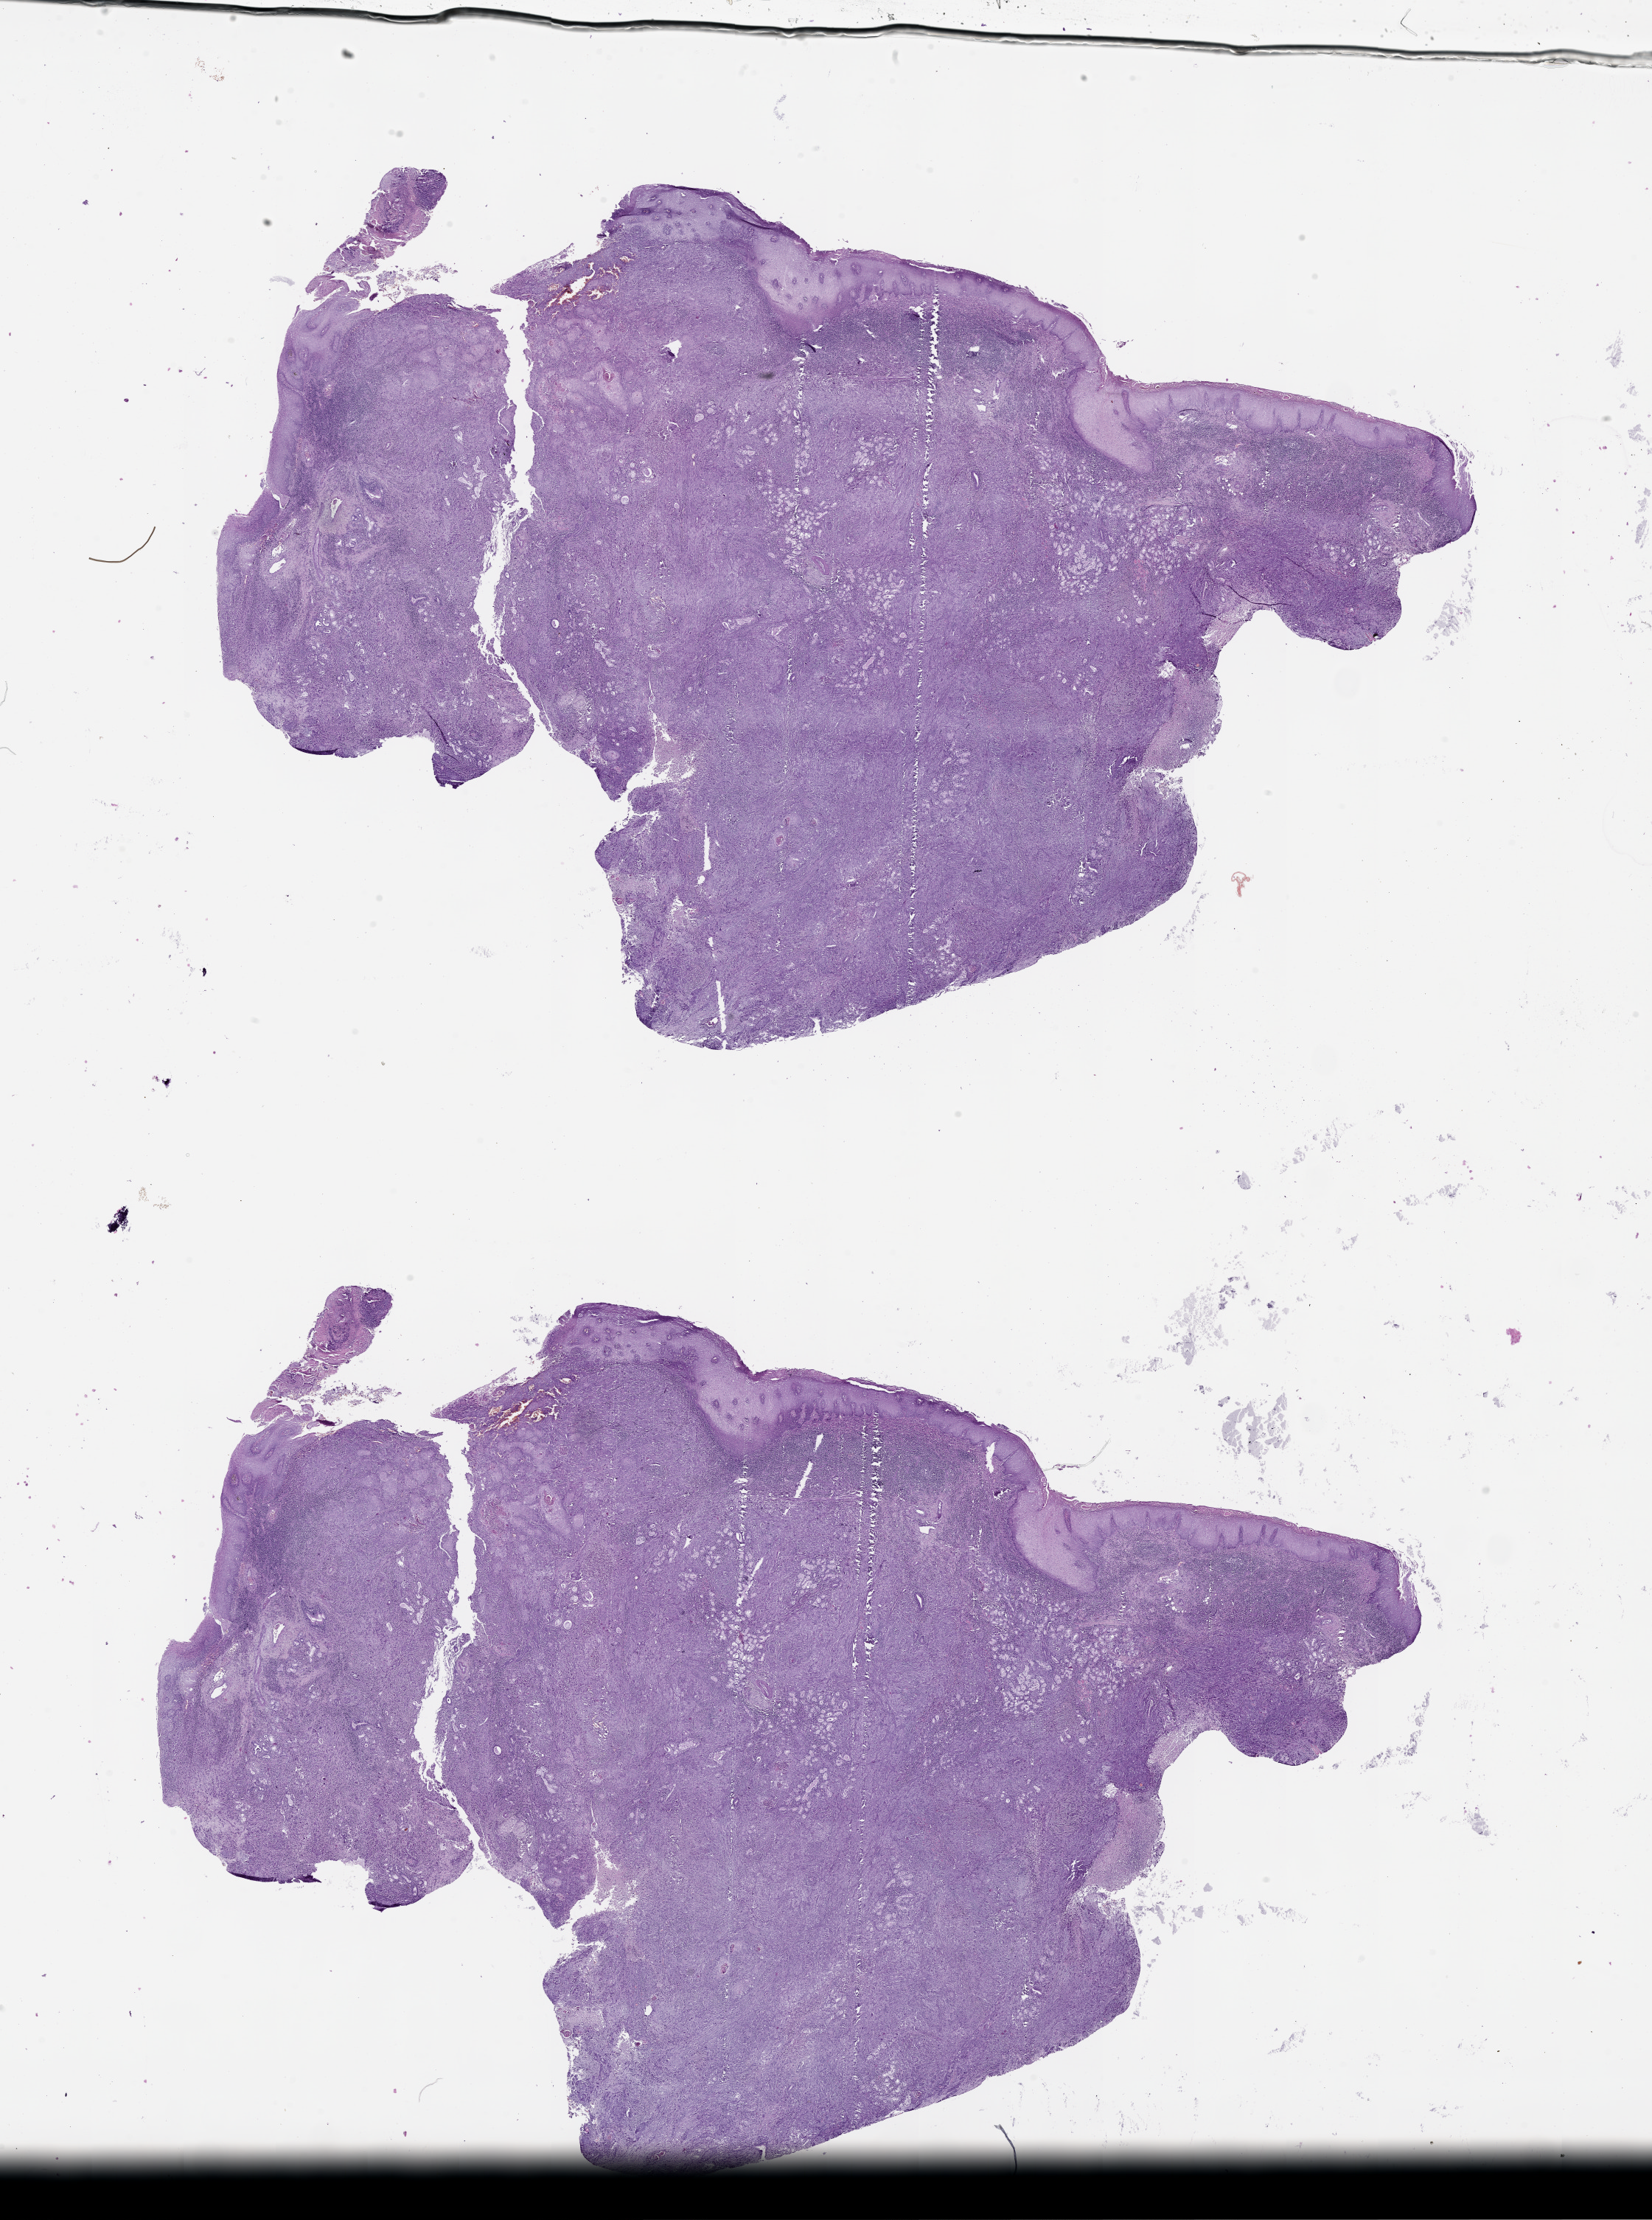
Whole-slide histology image, H&E, low-resolution overview of the scanned area, about 18.0 x 24.2 mm (acquisition: 20x scan). Head and neck, tissue type not recorded.
Patient diagnosis (cohort enrolment): head and neck cancer (head-neck).